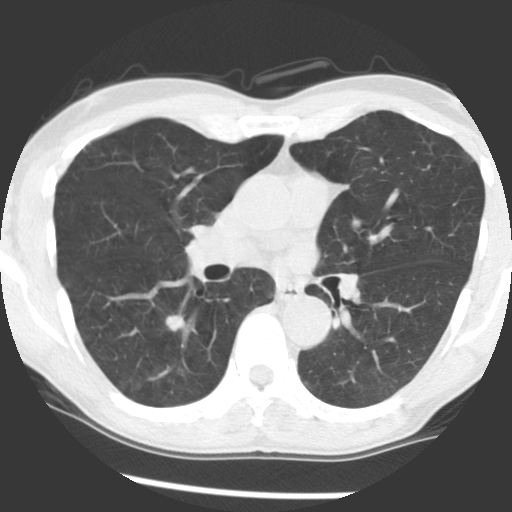
Low-dose screening chest CT, axial slice. First (baseline) screen. Lung window (W 1500 / L -600 HU). Standard (soft-tissue) reconstruction kernel (STANDARD). Male, age 65 years at enrolment.
Expert reader's lesion annotation, bounding box <147,299,204,344> (left, top, right, bottom; pixels). The screening reader recorded 2 non-calcified nodules or masses ≥4 mm on this exam (right lower lobe, left lower lobe); which of them this box marks is not recorded. Official screen result: positive, change unspecified: nodule(s) >= 4 mm or enlarging nodule(s), mass(es), or other non-specific abnormalities suspicious for lung cancer. Later outcome: lung cancer diagnosed 774 days after this screen — adenocarcinoma, NOS, right lower lobe, poorly differentiated (G3), stage IA (AJCC 6th edition), 18 mm at pathology.